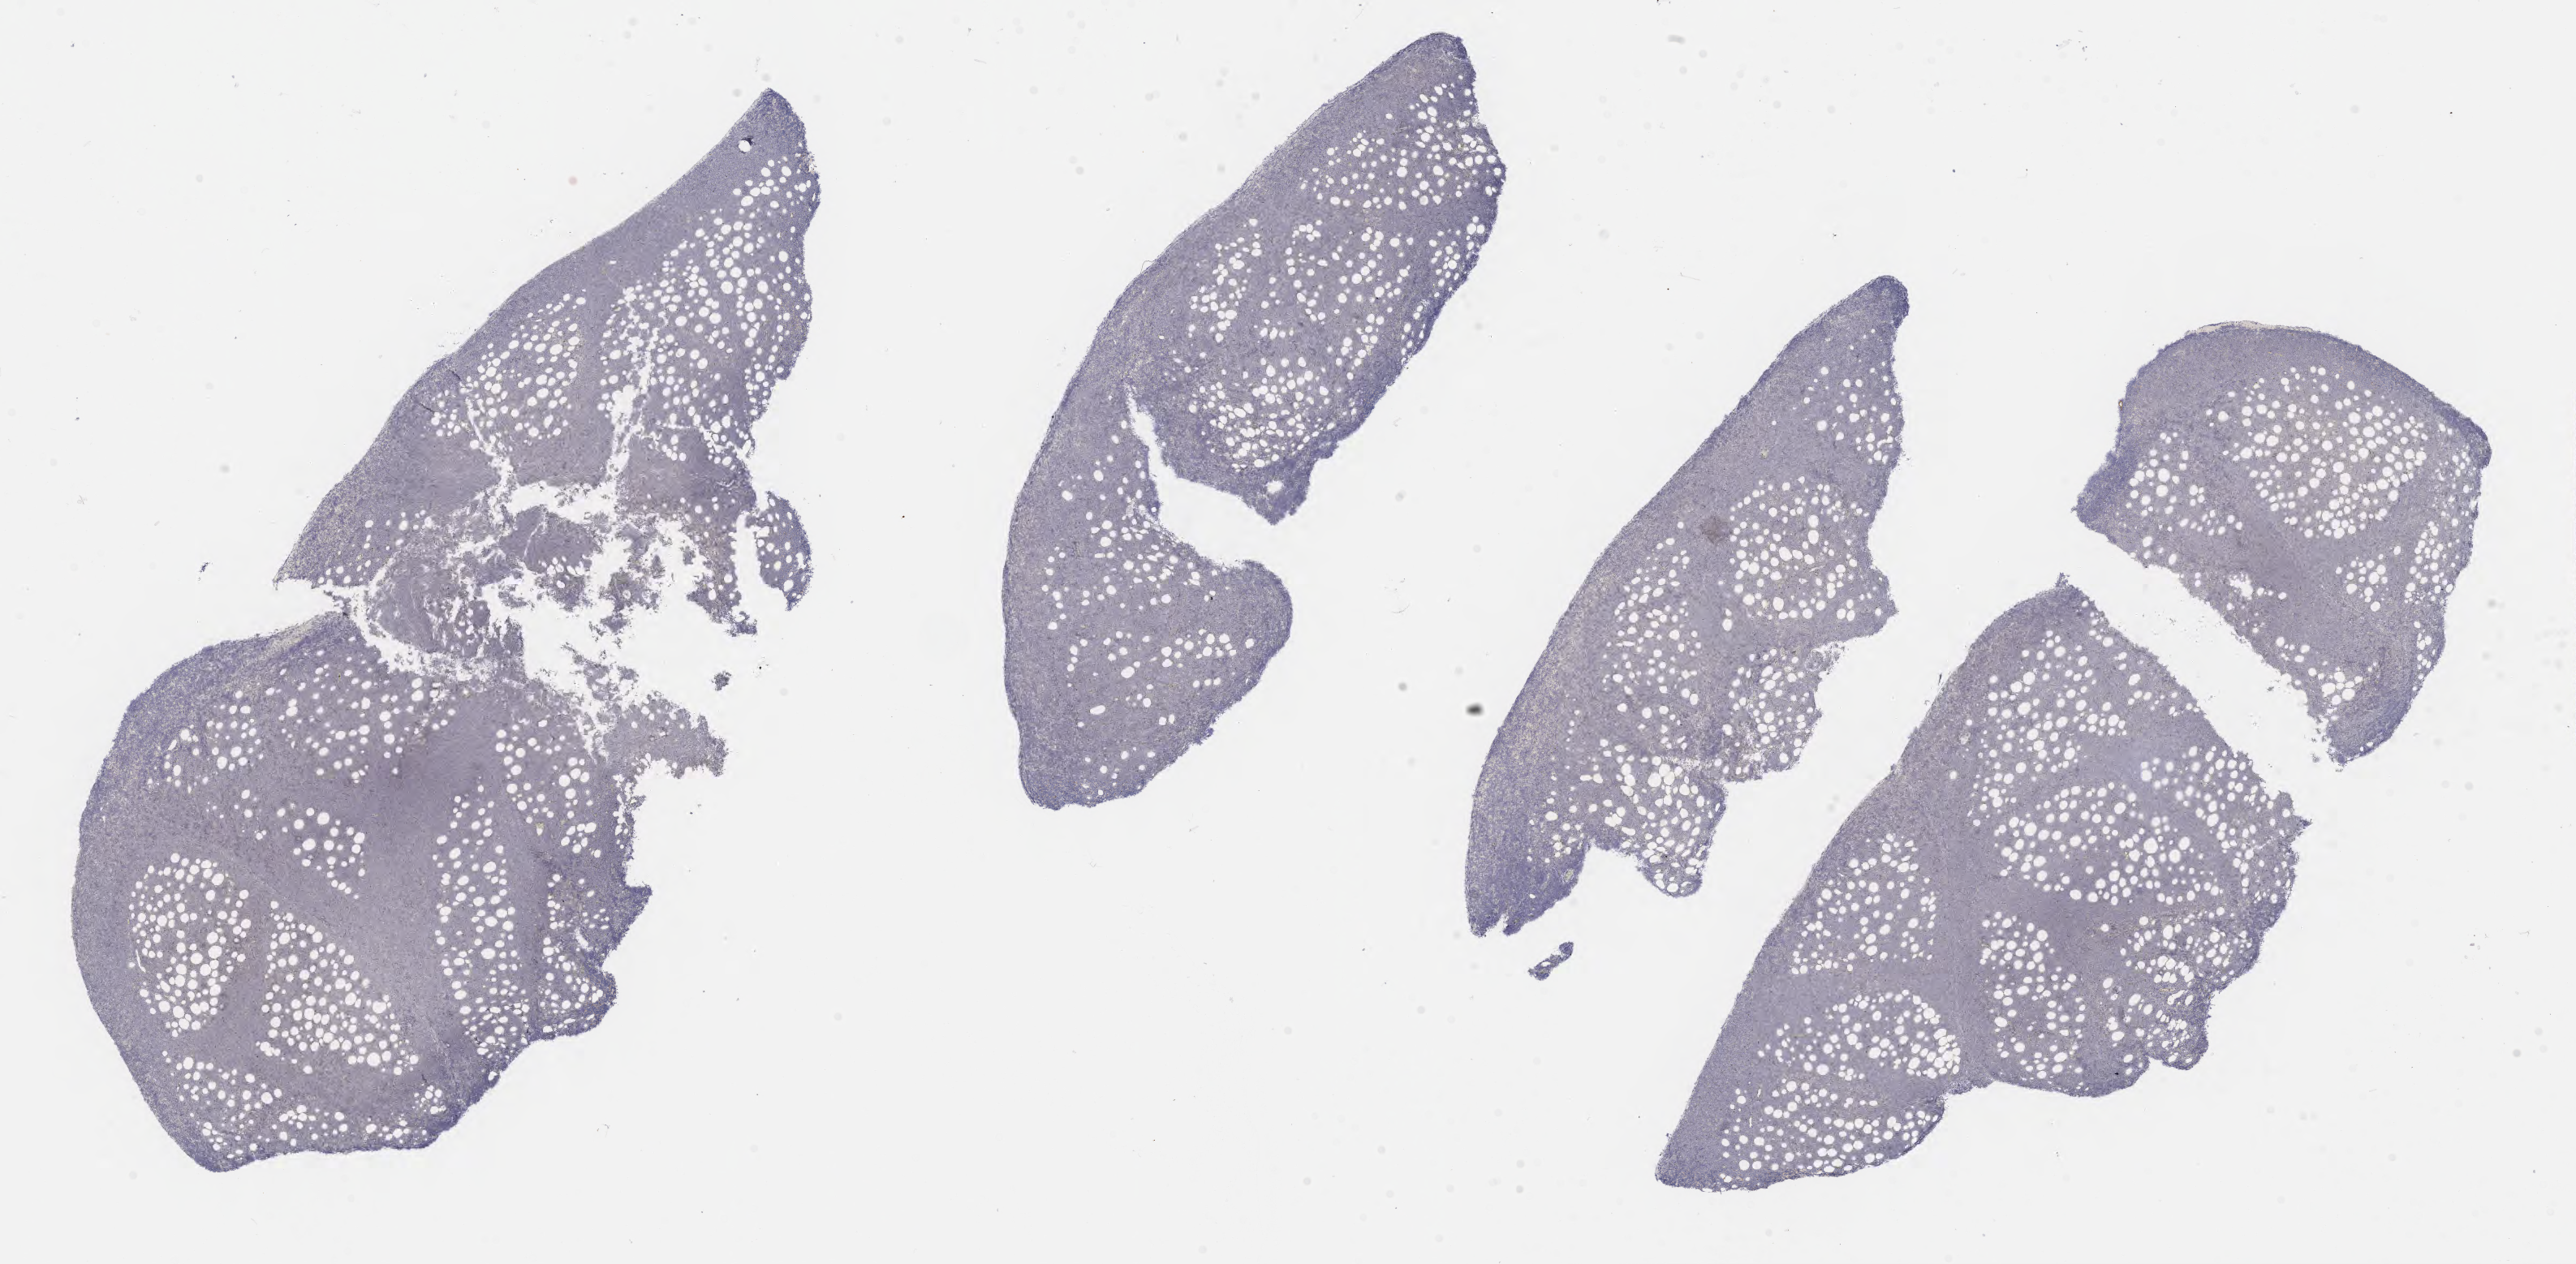
IHC for BCL2, whole-slide image — shown as a low-resolution overview of the whole scanned area (about 25.7 x 12.6 mm). Specimen: tumor tissue. Male patient, aged 52.
- histologic diagnosis: Diffuse large B-cell lymphoma, NOS